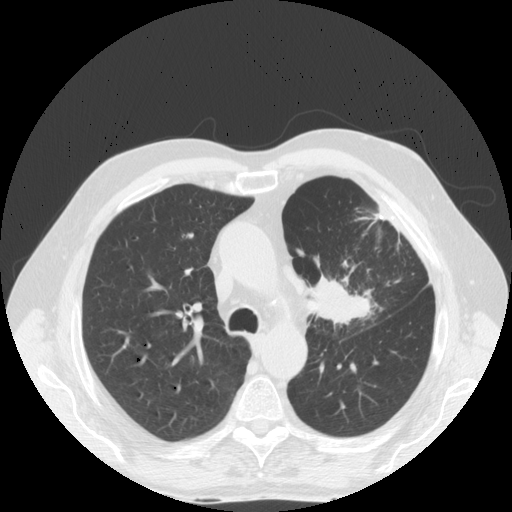
Low-dose screening chest CT, one axial slice. Slice 119 of 170 in the series (ordered by position). Lung window (W 1500 / L -600 HU). 2.5 mm slice thickness. 512 × 512 image matrix, field of view 380 × 380 mm.
Structures marked on this image (expert manual segmentation):
- lesion 1 (tumor, upper lobe of left lung): bounding box <308,275,378,326> (left, top, right, bottom; pixels)